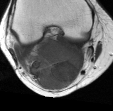
MRI of an extremity soft-tissue mass, one axial slice; position 18 of 45 along the scan axis; MR volume resampled by the dataset authors to the PET/CT grid (not the native acquisition matrix); 113 × 111 image matrix, field of view 110 × 108 mm. Female patient. From the clinical record (not read from this slice): histological type: liposarcoma; site of the primary tumour: right thigh.
Annotated regions visible in this slice (expert contour drawn on MRI and transferred to this co-registered scan by the dataset authors):
- gross tumour volume (mass): bounding box <26,35,84,91> (left, top, right, bottom; pixels)